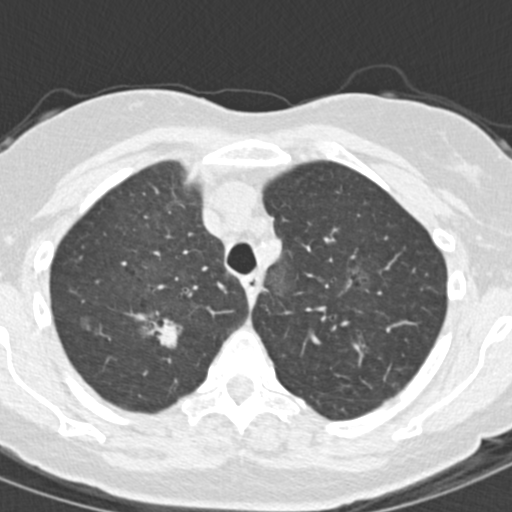
Low-dose screening chest CT, one axial slice. Slice 119 of 157 in the series (ordered by position). Lung window (W 1500 / L -600 HU). 512 × 512 image matrix.
Annotated regions visible in this slice (manually delineated by an expert):
- lesion 1 (tumor, upper lobe of right lung): bounding box <139,316,183,359> (left, top, right, bottom; pixels)